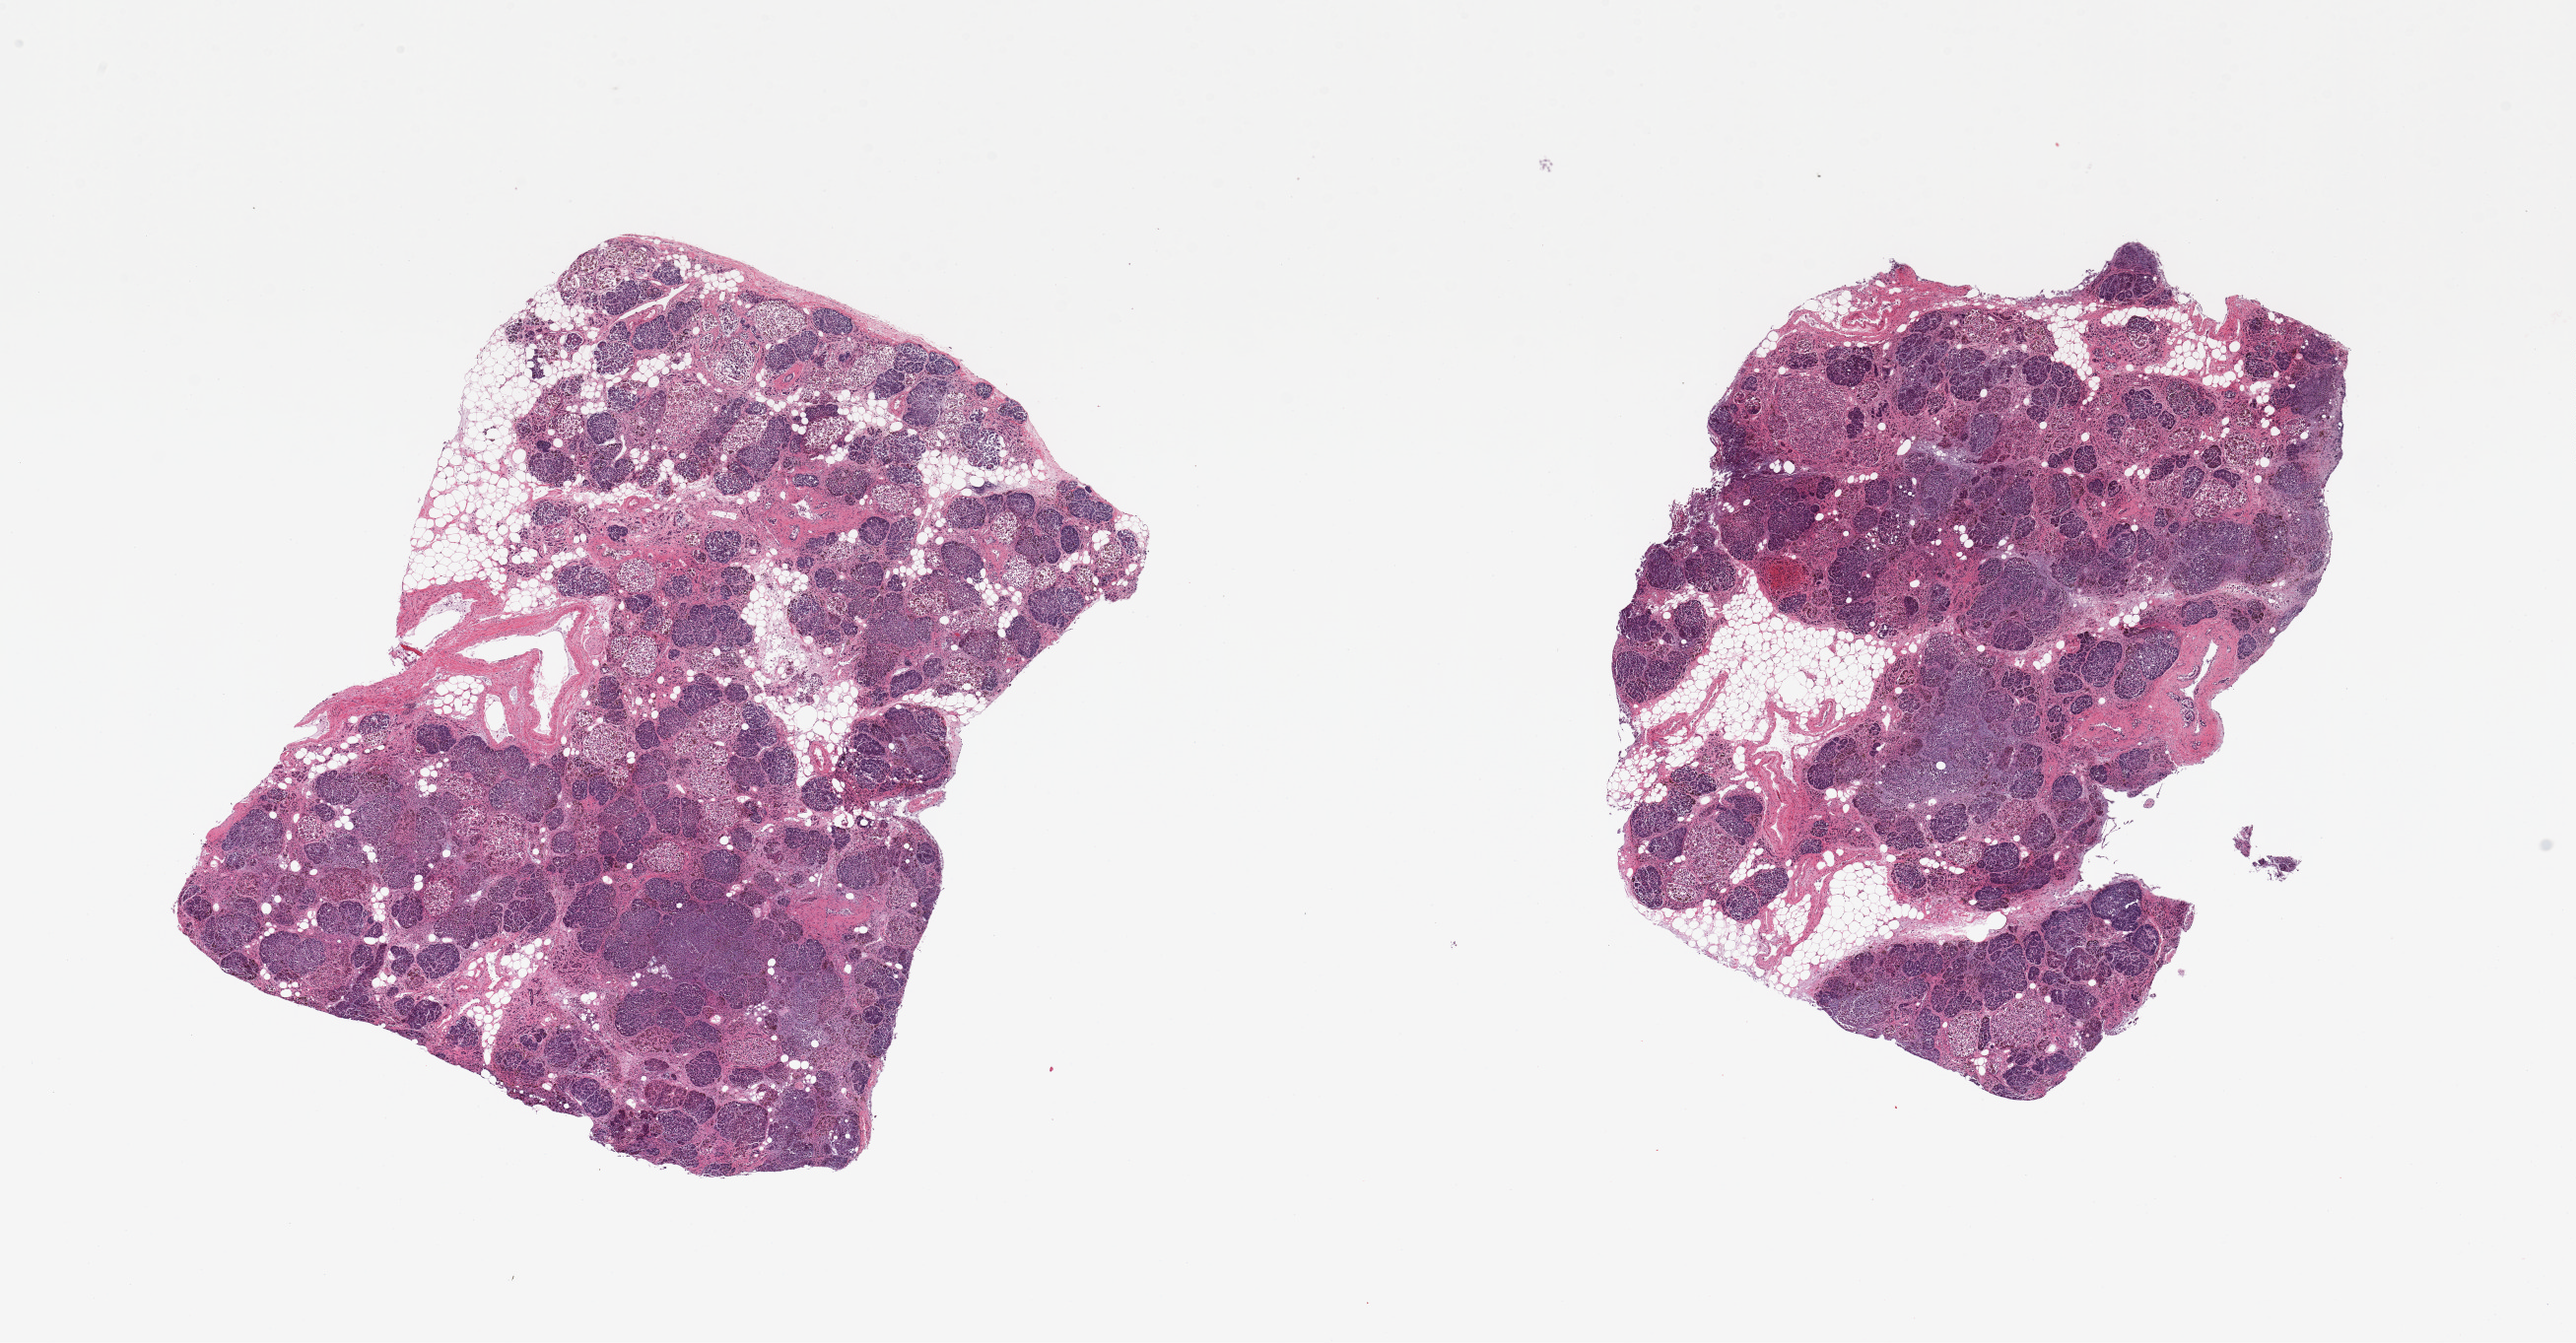
Whole-slide image, hematoxylin and eosin (H&E) stain, brightfield, low-resolution overview of the scanned area, about 20.7 x 10.8 mm (slide scanned at 20x). PAXgene-fixed, paraffin-embedded tissue. Section of pancreas (target tissue). Donor tissue sample. Donor sex: female.
Reviewer comment on this tissue sample: 2 pieces; high islet content (40%); 20% internal fat content.